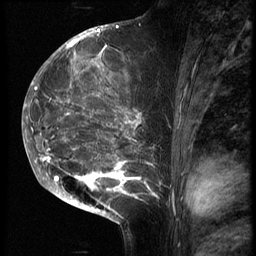
Breast MRI (dynamic contrast-enhanced), one sagittal slice. Position 33 of 70 along the scan axis. 3 images stored at this slice position (order not interpretable as contrast timing). 1.5 T. TE 4.2 ms, TR 9 ms. 2.5 mm slice thickness. 256 × 256 image matrix, field of view 180 × 180 mm. Female patient, age 28 years. From the clinical record (not read from this slice): setting: breast cancer imaged before/during neoadjuvant chemotherapy.
Outlined on this slice (semi-automatically segmented with operator editing):
- analysis volume of interest (the breast-tissue region the enhancement analysis was run in; not a lesion): bounding box [x1, y1, x2, y2] px = [43, 42, 169, 215]
- tumour enhancement mask (voxels above the 140 % enhancement threshold inside the analysis volume of interest): [43, 42, 159, 204]